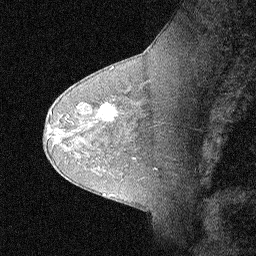
Breast MRI (dynamic contrast-enhanced), one sagittal slice; slice 45 of 64 in the series (ordered by position); dynamic contrast-enhanced study with each time point stored as its own series, time point 2 of 3 at this slice position (early post-contrast, ordered by acquisition time); 1.5 T; TE 4.5 ms, TR 11 ms; 2.06 mm slice thickness; 256 × 256 image matrix, field of view 200 × 200 mm. Female patient, age 62 years. From the clinical record (not read from this slice): setting: breast cancer imaged before/during neoadjuvant chemotherapy; receptor status: HR-positive, HER2-negative.
Outlined on this slice (semi-automatically segmented with operator editing):
- analysis volume of interest (the breast-tissue region the enhancement analysis was run in; not a lesion): bounding box (x1, y1, x2, y2) in pixels: (91, 93, 124, 129)
- tumour enhancement mask (voxels above the 90 % enhancement threshold inside the analysis volume of interest): (92, 95, 115, 119)